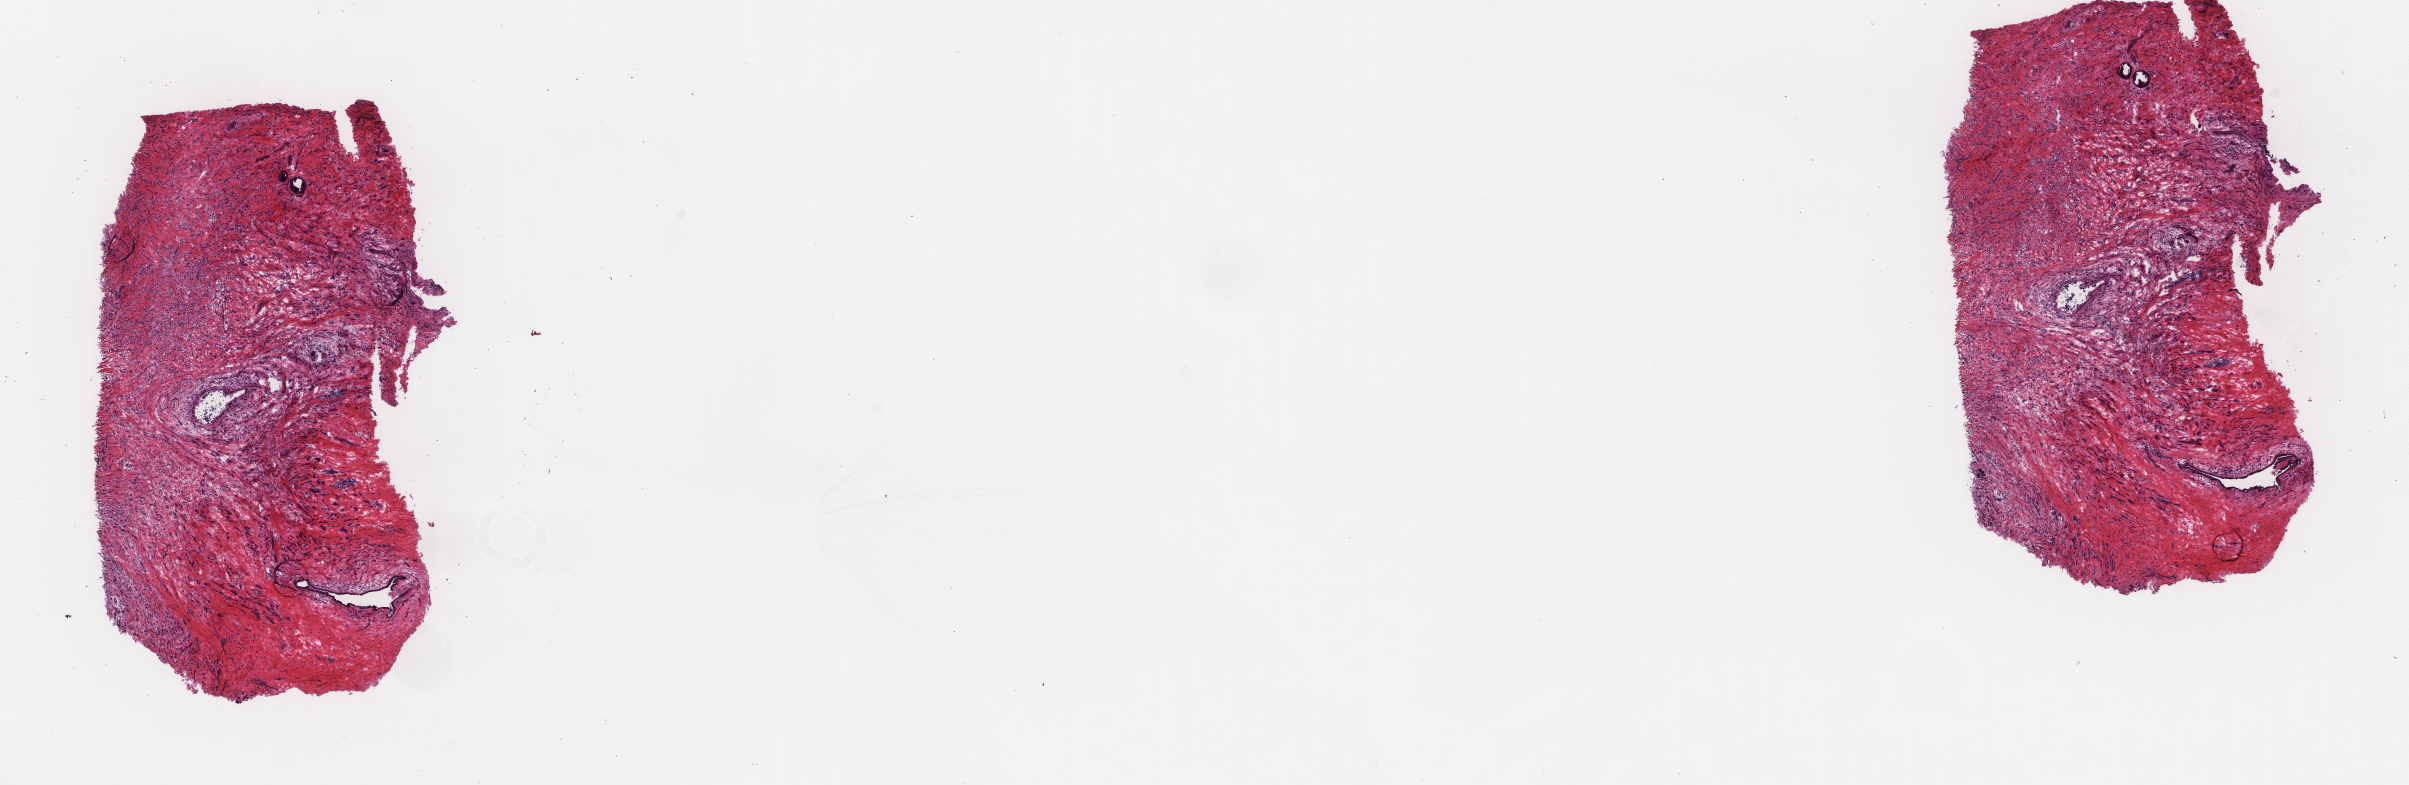
H&E whole-slide image, low-resolution overview of the scanned area, about 19.1 x 6.2 mm (from a 40x scan). Frozen section. Sample: primary tumour, breast. Female patient; age at initial diagnosis 44 years. Pathologist review of this section (percent, as recorded): tumour cells 70%, tumour nuclei 80%, normal cells 2%, stromal cells 28%, necrosis 0%. Infiltration values recorded for this section: lymphocyte infiltration 1%, monocyte infiltration 0%, neutrophil infiltration 0%.
* laterality: left
* AJCC pathologic stage: IIA (6th edition)
* diagnosis: Lobular carcinoma, NOS
* lymph nodes positive (case pathology): 0 of 14 examined